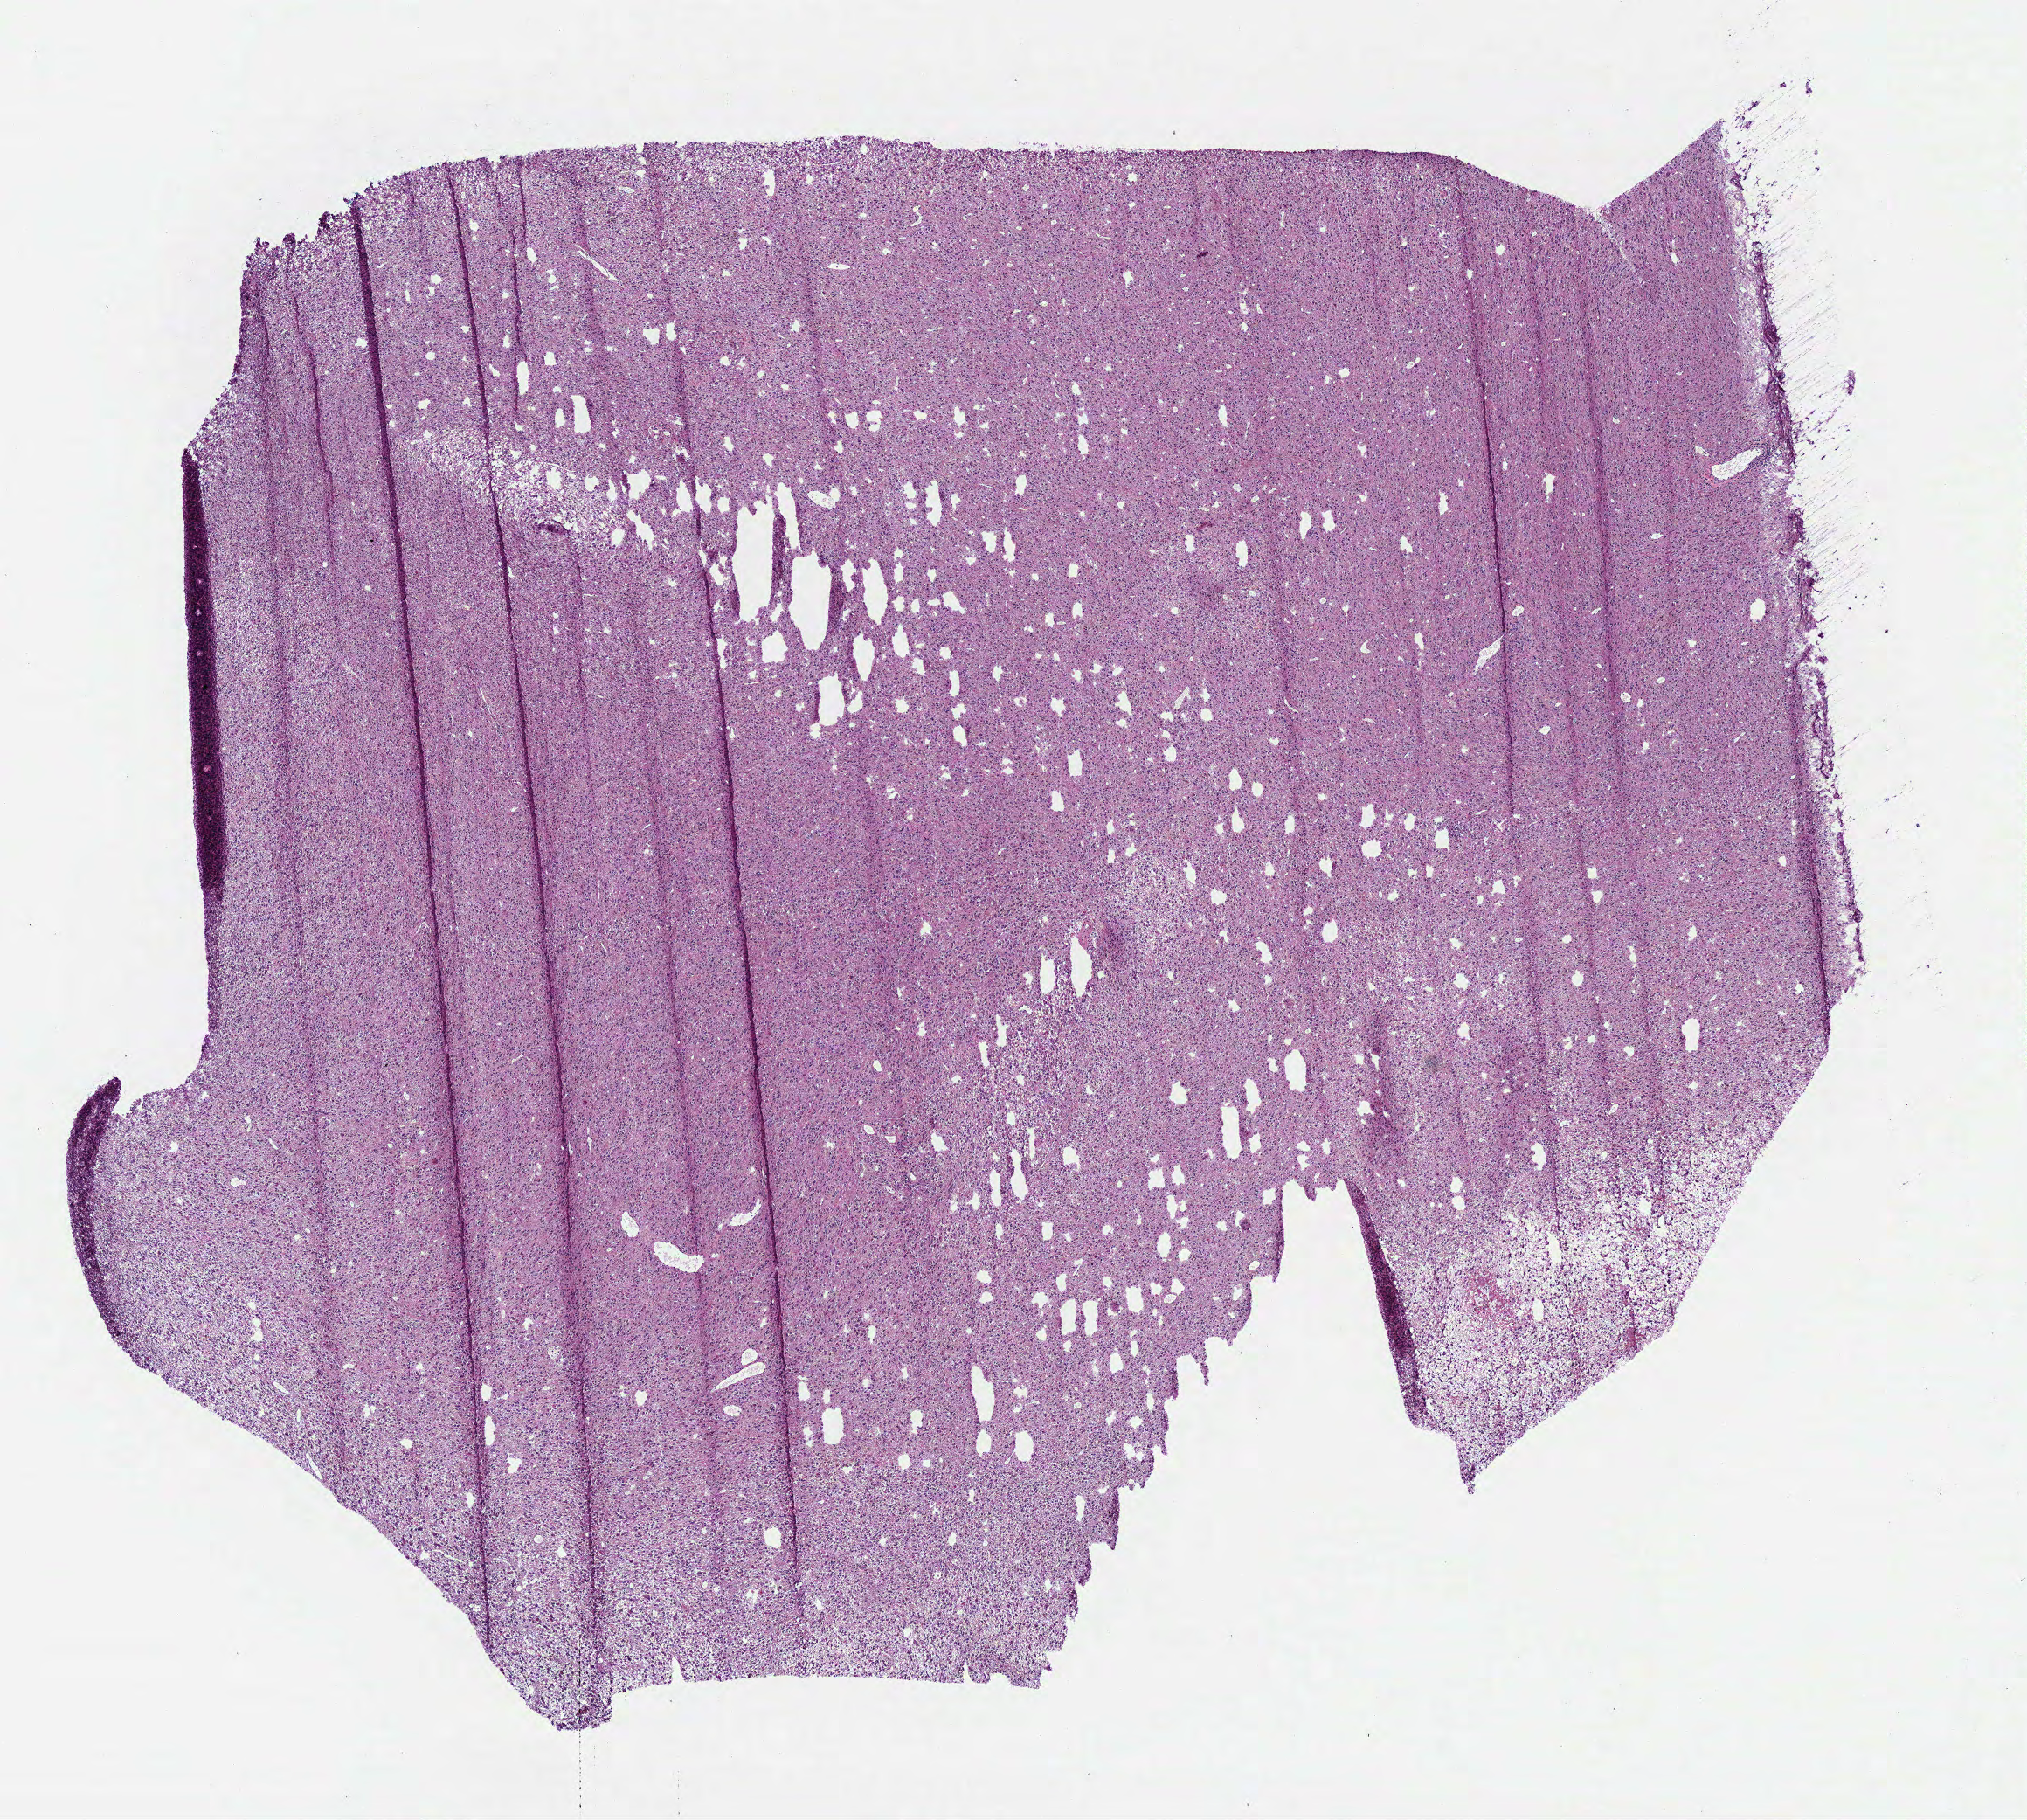
Whole-slide histology image, H&E-stained — shown as a low-resolution overview of the whole scanned area (about 9.1 x 8.2 mm, from a 40x scan); frozen section; primary tumour sample from the brain. Male, age 63 years at initial diagnosis. Composition of this section per pathologist review: tumour cells 100%, tumour nuclei 85%, normal cells 0%, stromal cells 0%, necrosis 0%.
Histologic diagnosis: Glioblastoma.